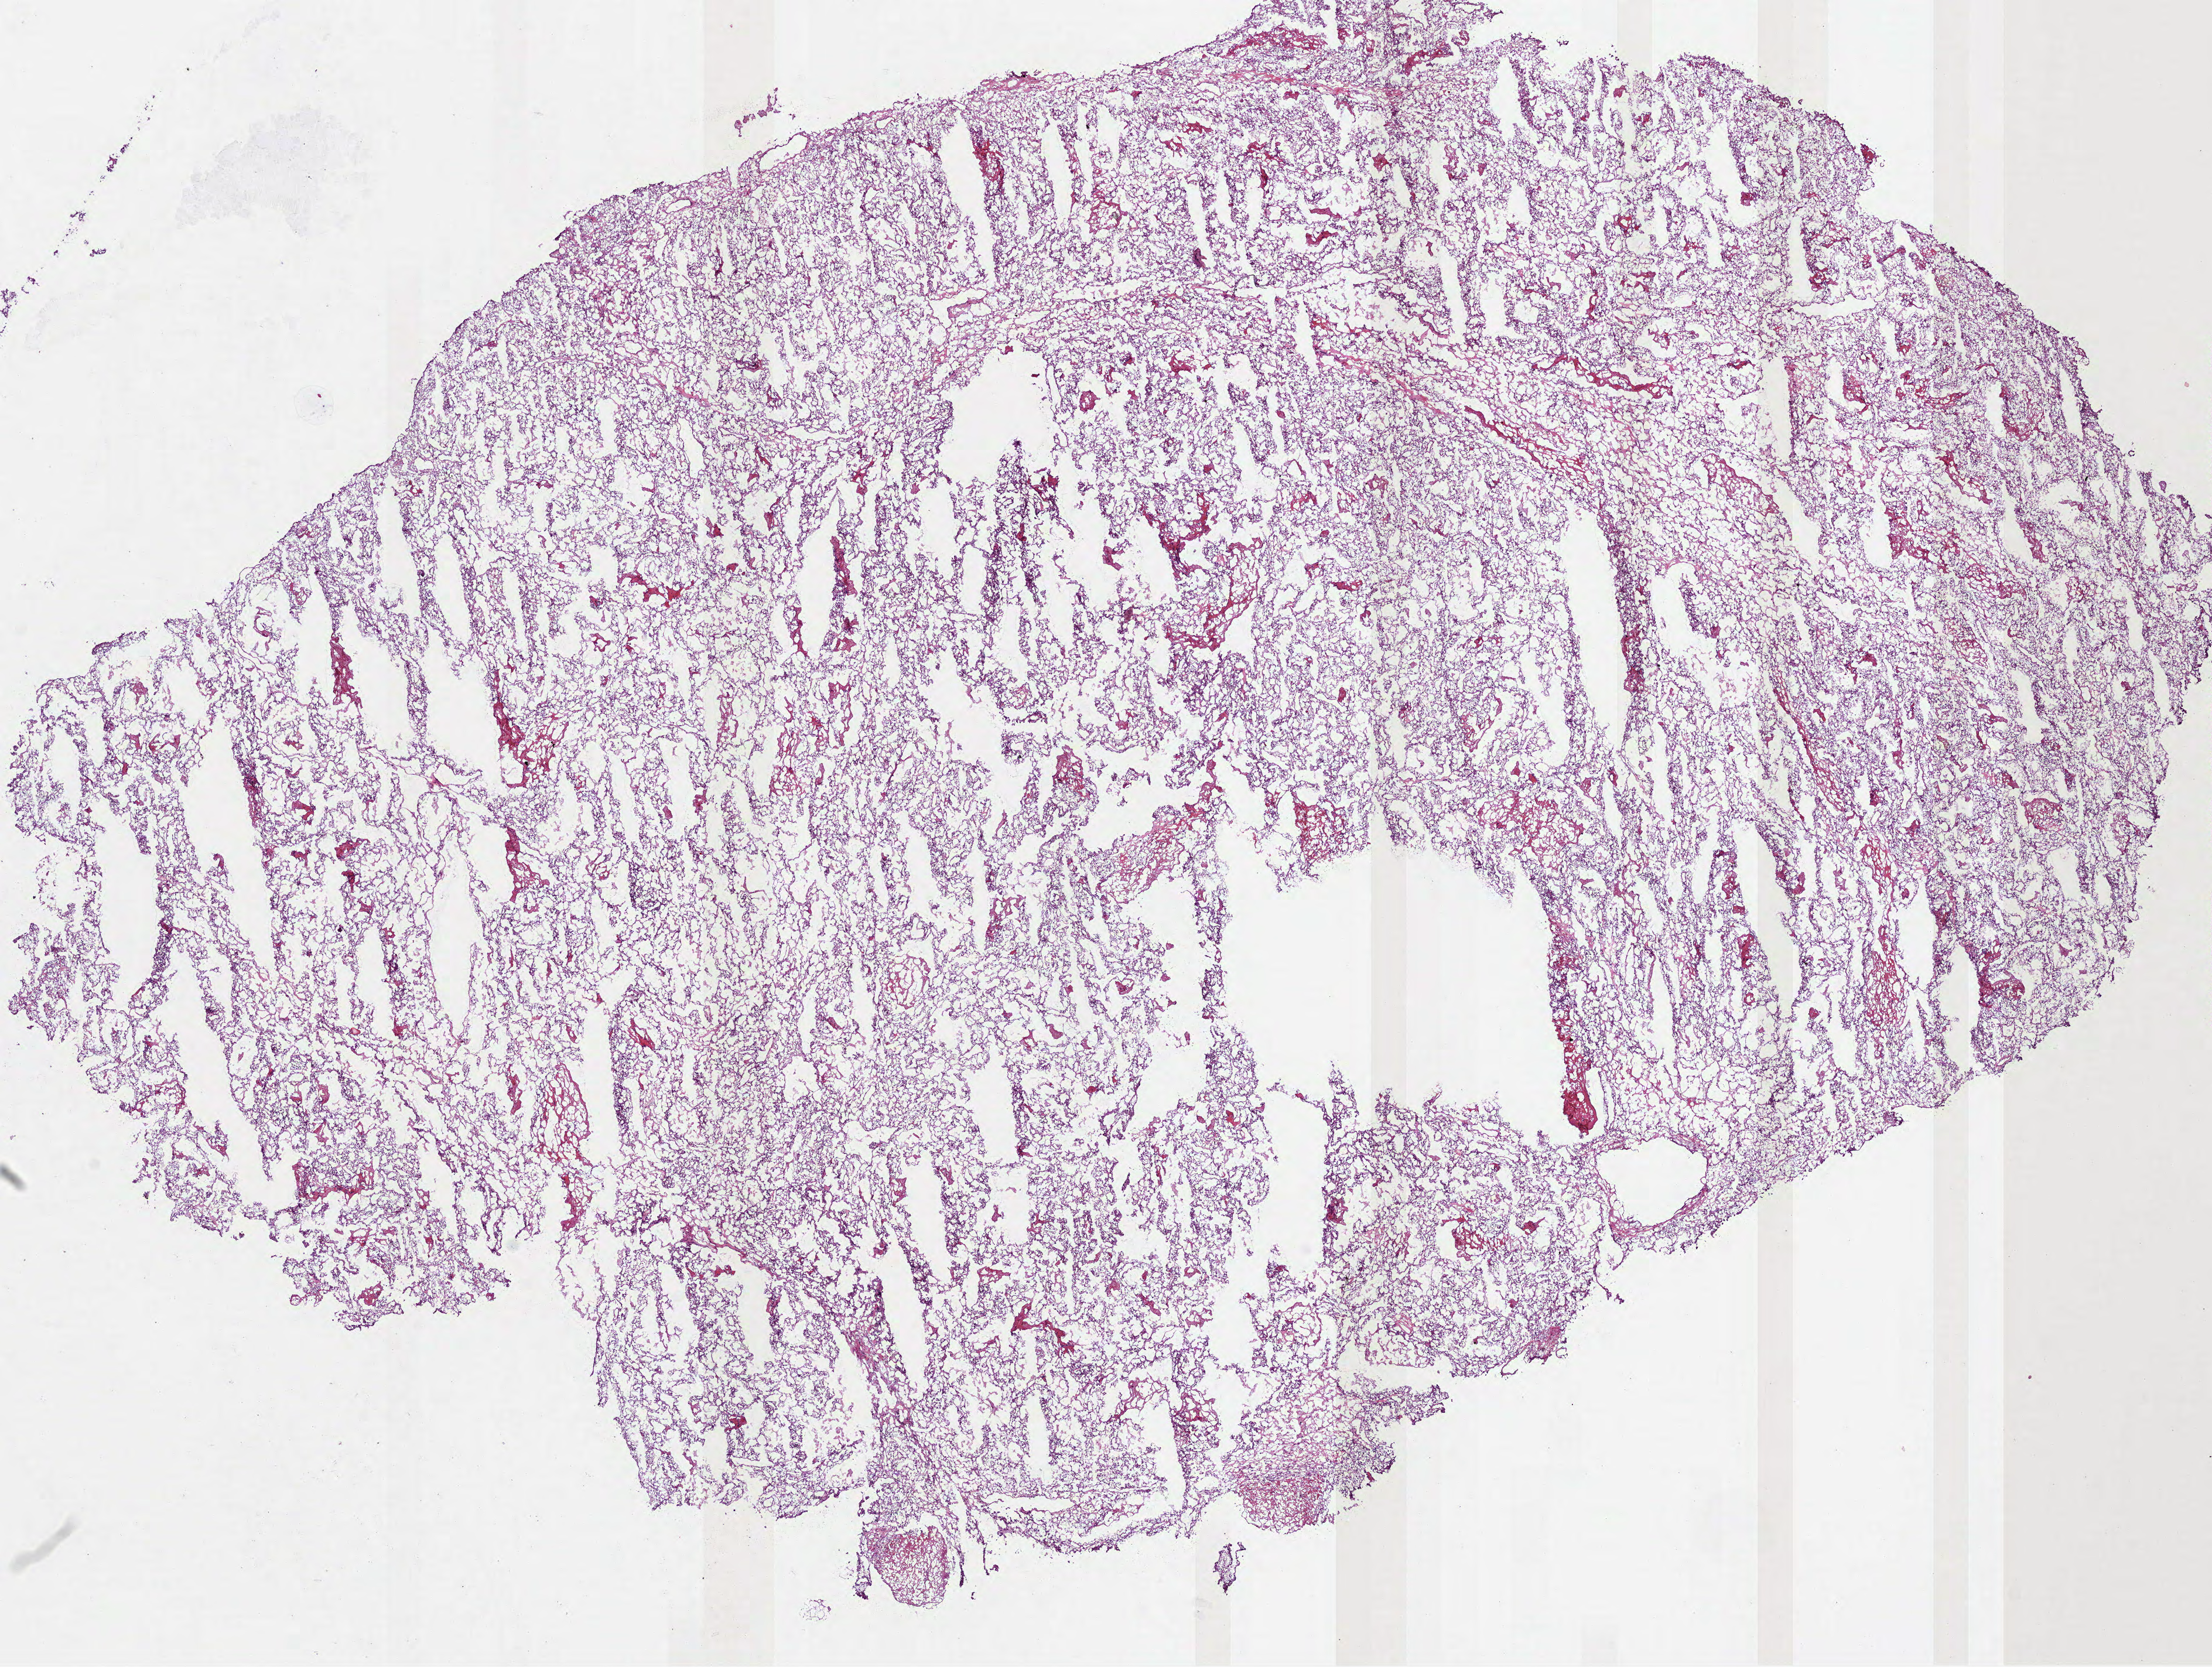
Digitized Hematoxylin and eosin (H&E) stained tissue section (whole slide) — shown as a low-resolution overview of the whole scanned area (about 15.2 x 11.5 mm, from a 40x scan). Frozen section from the bottom of the tissue portion. Sample: primary tumour, kidney. Male patient; age at initial diagnosis 38 years.
Histologic diagnosis: Clear cell adenocarcinoma, NOS.